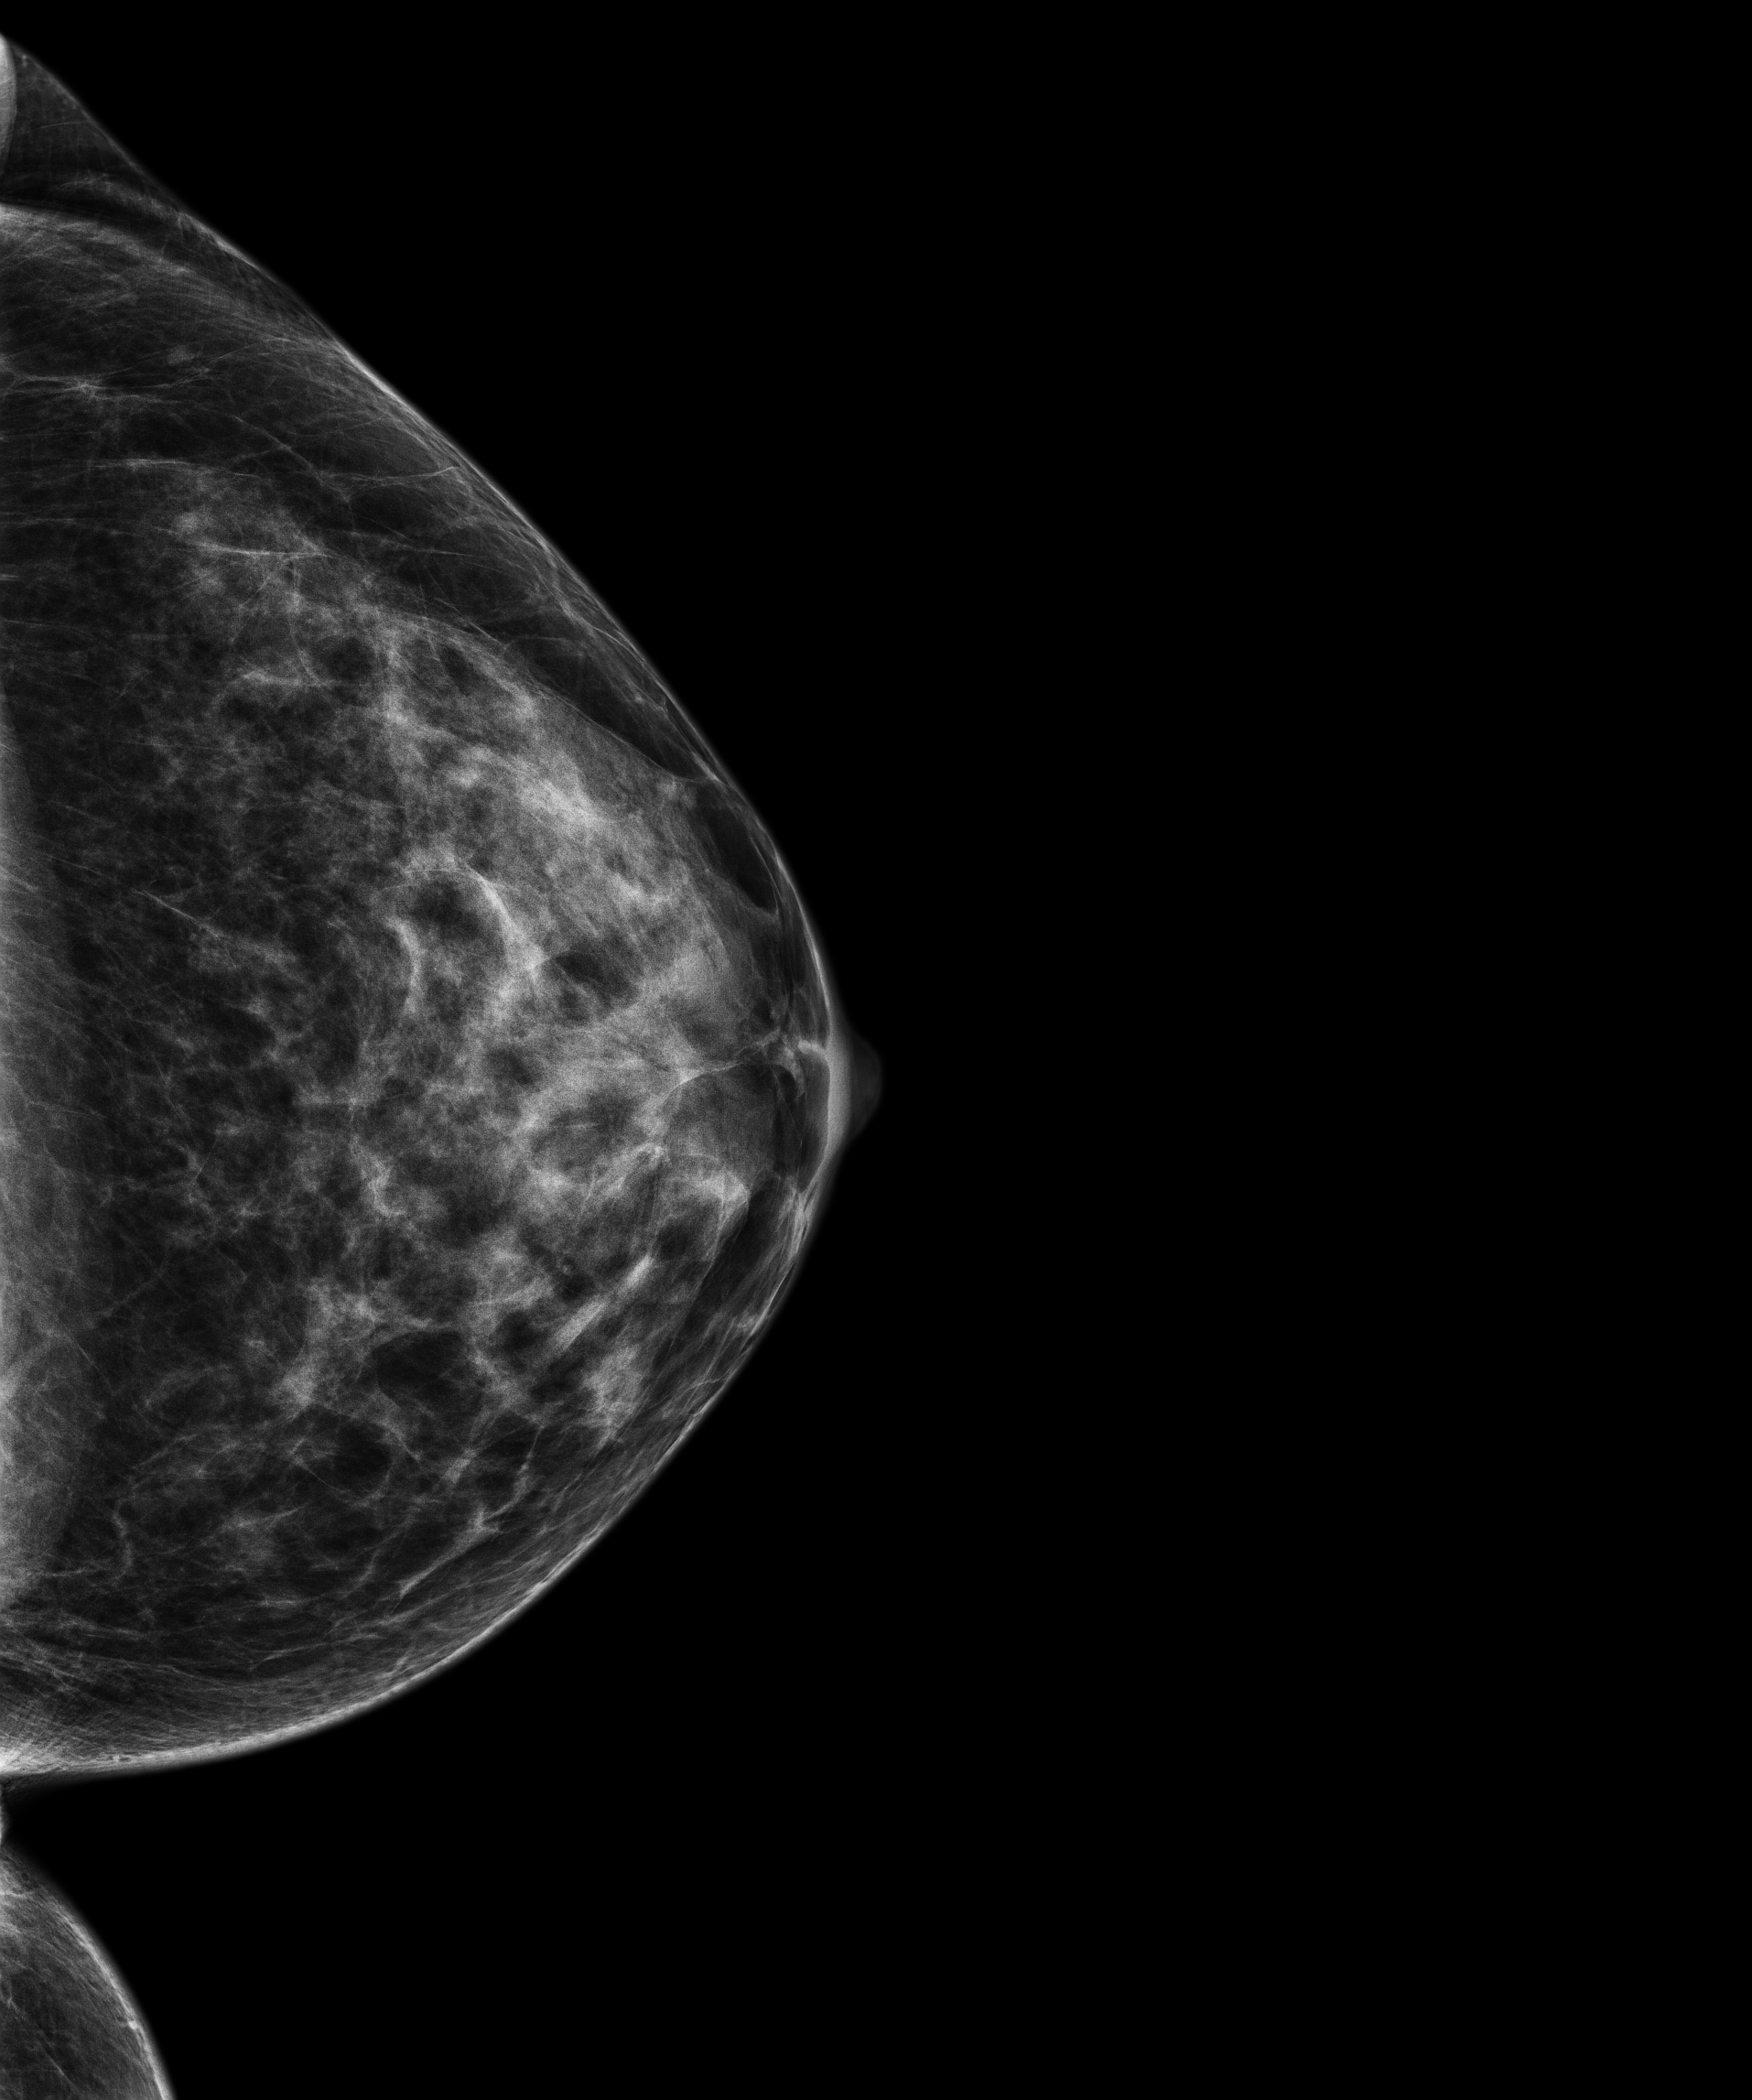
Annual screening mammography examination; system: Senographe Pristina. Patient: female, 43 years.
Image type: full-field digital mammogram. Breast: left. Projection: cranio-caudal projection.